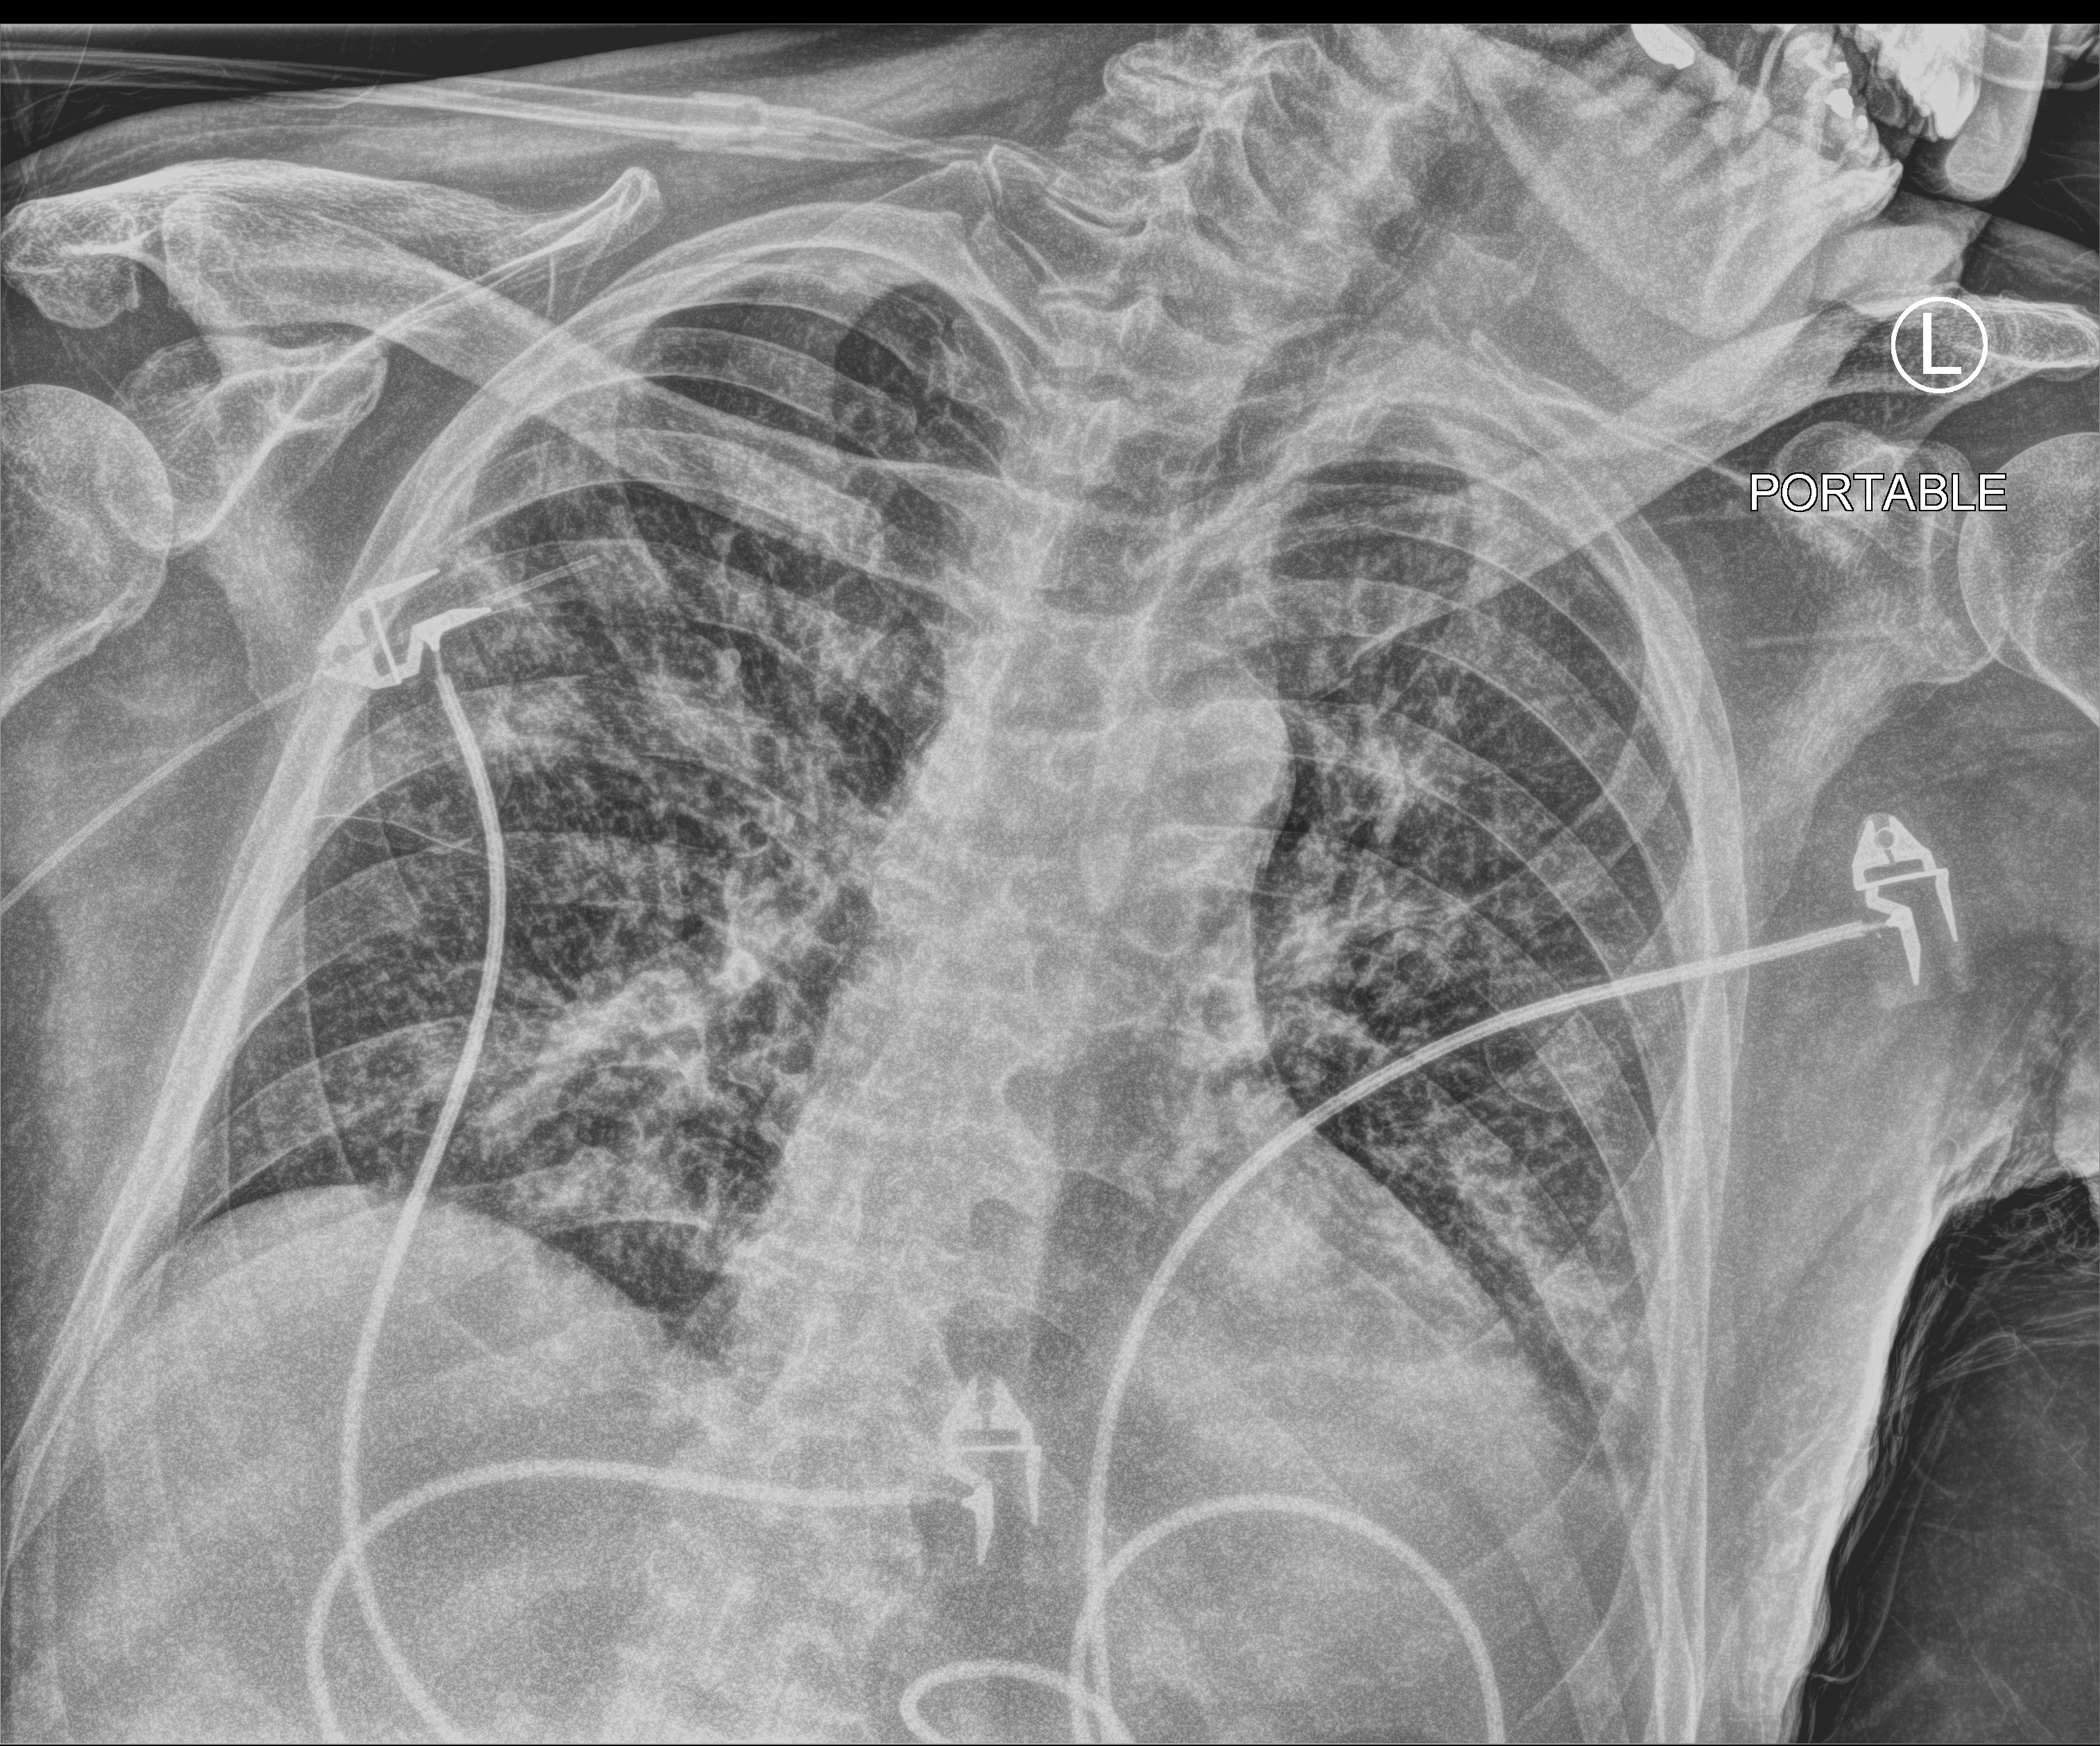
Portable chest radiograph, anteroposterior (AP) projection. Patient hospitalised with COVID-19; male, aged 60–74 years.
From the hospital-stay record, not from the radiograph (when in the stay this image was taken is not recorded): mechanically ventilated during this hospital stay: yes.